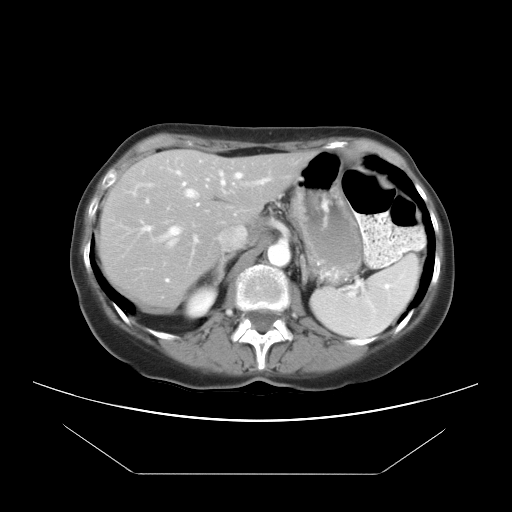
Contrast-enhanced abdominal CT, one axial slice; position 15 of 21 along the scan axis; reconstruction kernel STANDARD; 120 kVp; soft-tissue window (W 400 / L 40 HU); 512 × 512 image matrix, field of view 392 × 392 mm. Female patient, age 72 years. From the clinical record (not read from this slice): diagnosis: colorectal cancer liver metastases, imaged before liver resection; multiple liver metastases: yes; largest metastasis: 4 cm; disease in both lobes: yes.
Structures marked on this image (manually delineated by an expert):
- hepatic veins: box from (x=160, y=173) to (x=243, y=247) px
- liver: (x=101, y=152)–(x=310, y=309)
- planned liver remnant (the part of the liver to remain after resection): (x=101, y=152)–(x=309, y=280)
- portal vein (with intrahepatic branches): (x=141, y=179)–(x=267, y=242)
- liver metastasis: (x=190, y=263)–(x=201, y=273)